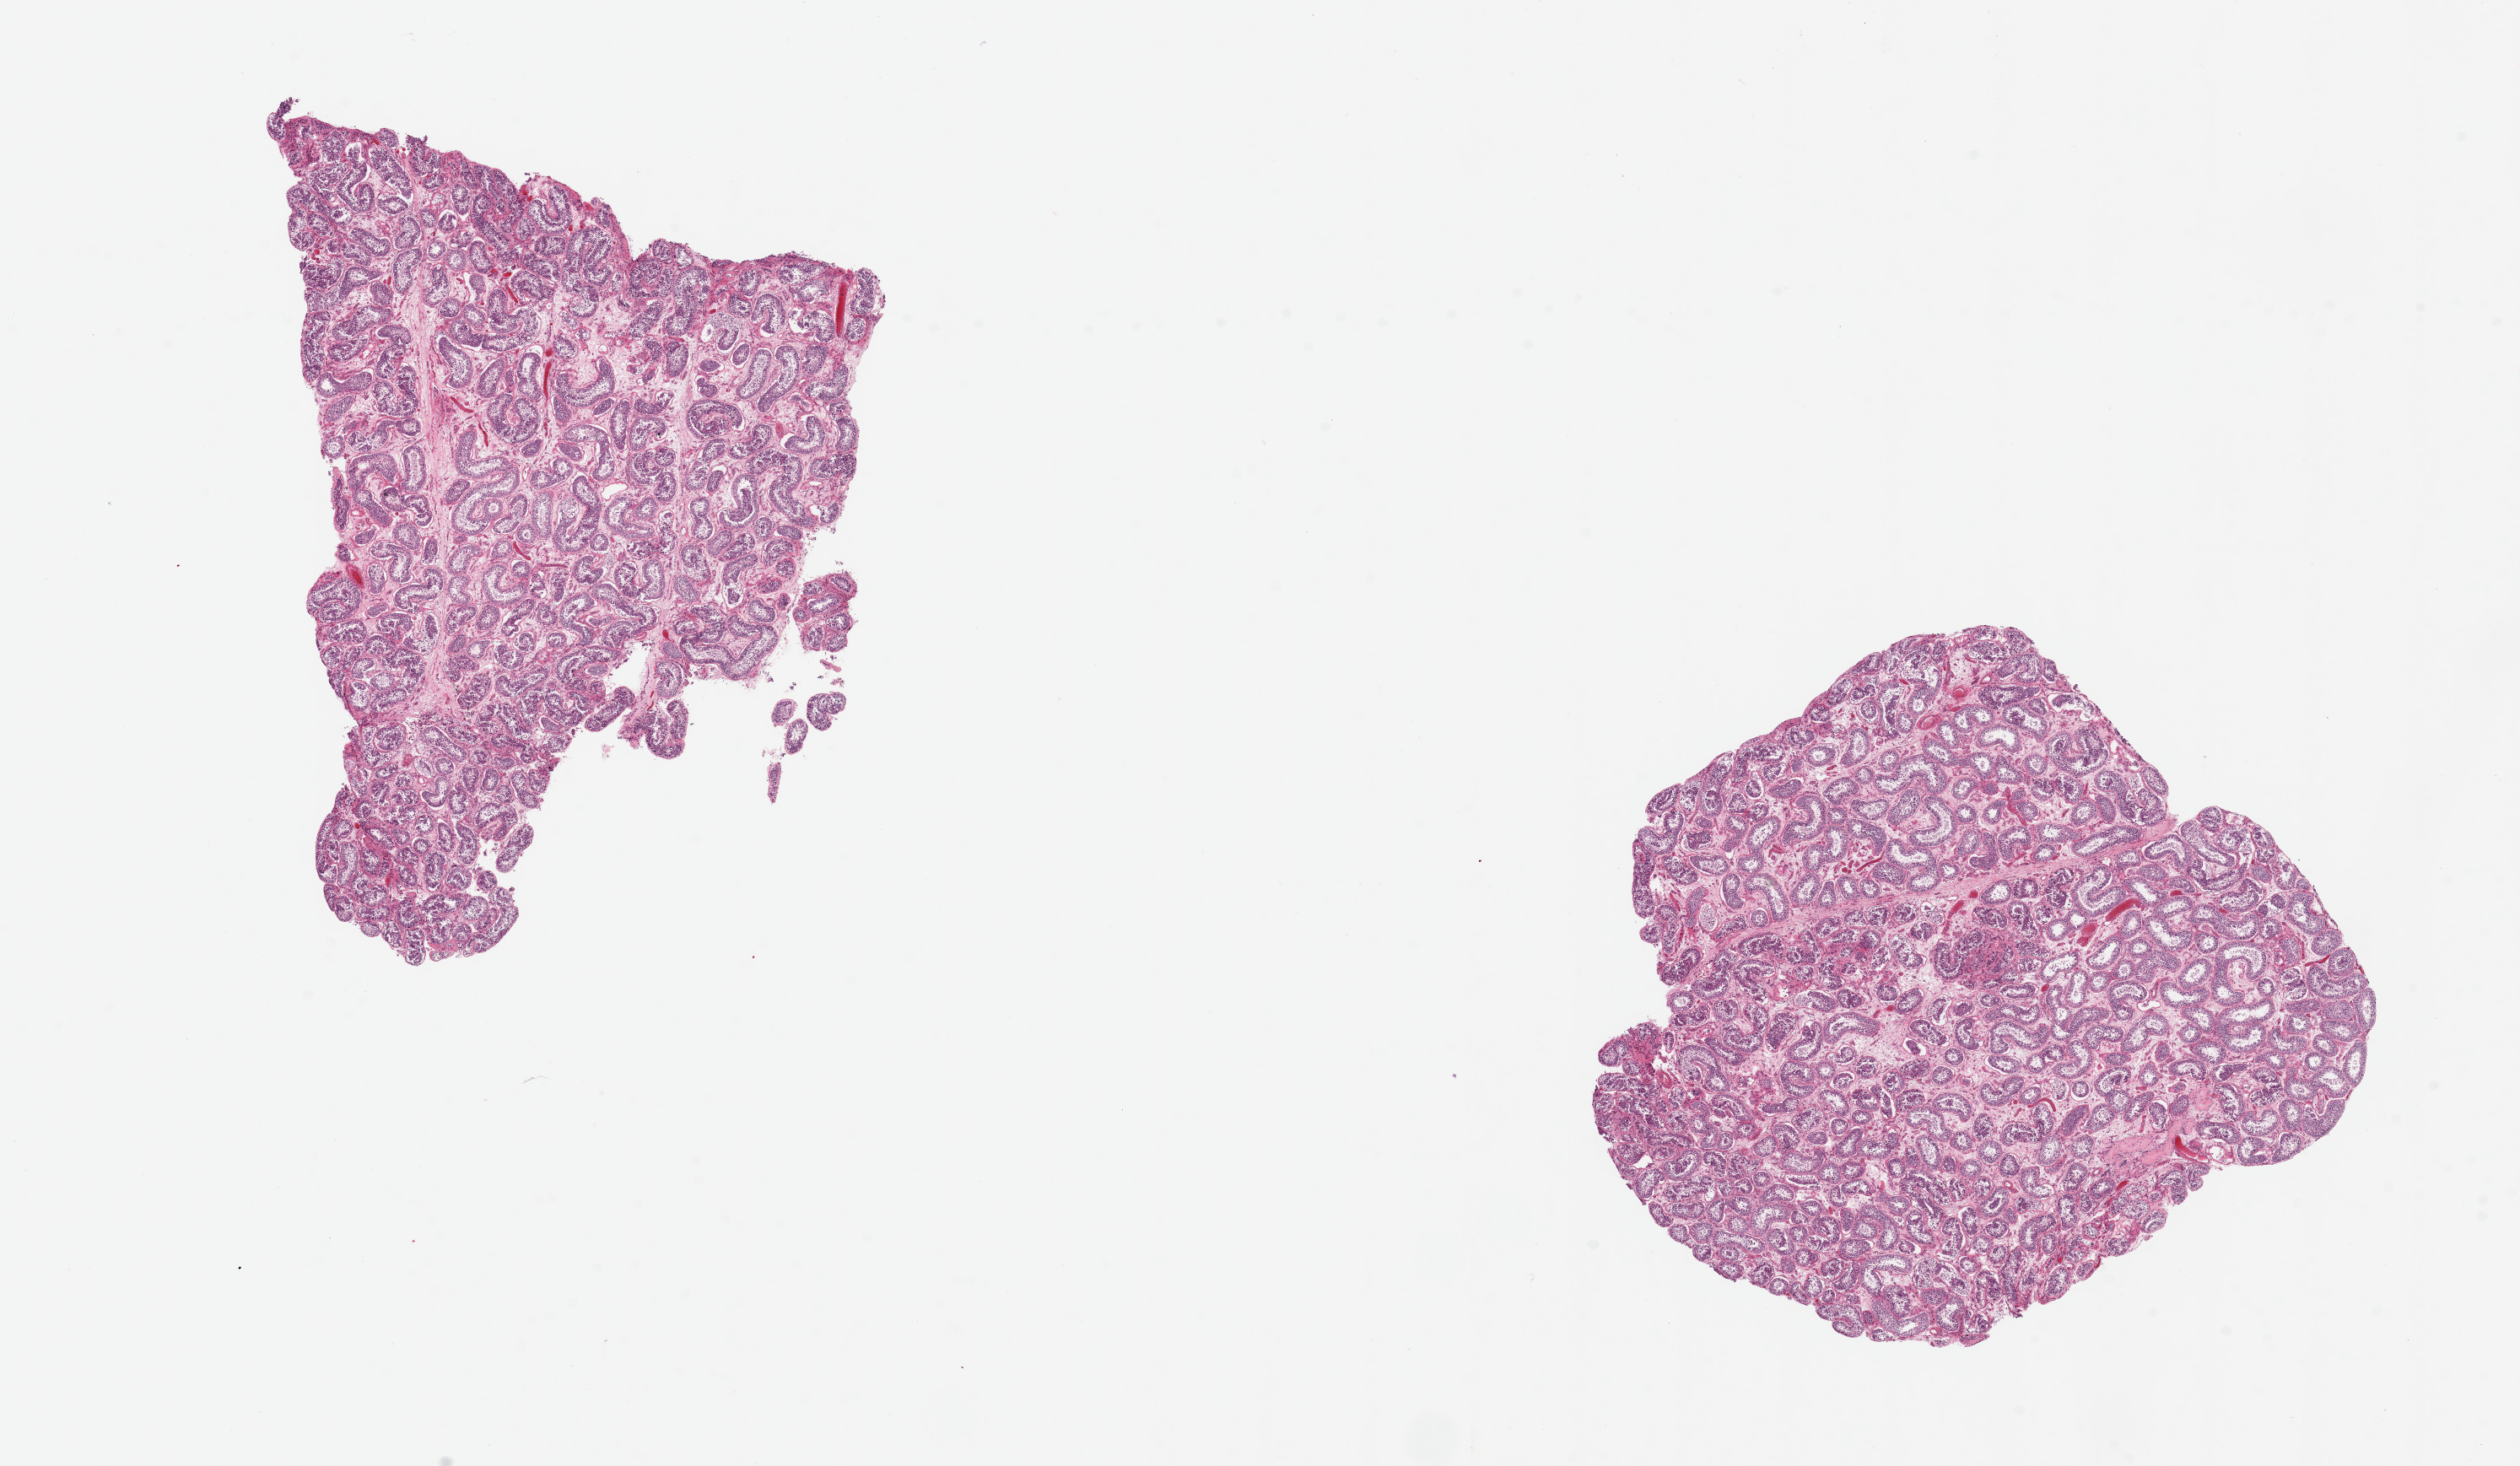
Hematoxylin and eosin (H&E) whole-slide image — shown as a low-resolution overview of the whole scanned area (about 23.6 x 13.7 mm, slide scanned at 20x). PAXgene-fixed paraffin-embedded (PFPE) section. Section of testis (target tissue). Donor tissue sample. Donor sex: male.
Review note (as recorded): 2 pieces ~7x6mm. Spermatogenesis present but appears reduced for young age of patient.